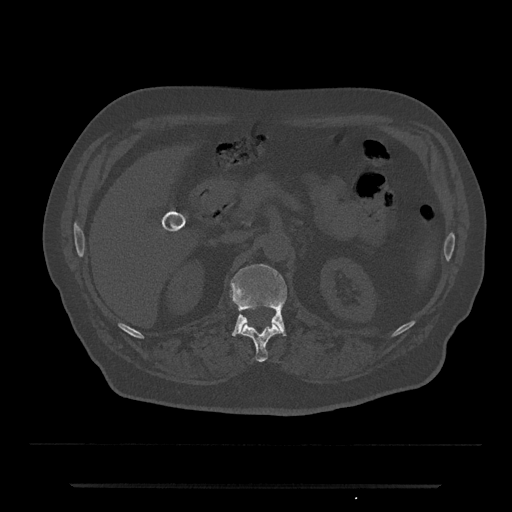
CT including the spine, one axial slice. Reconstruction kernel Br40s/3. Bone window (W 1800 / L 400 HU). 512 × 512 image matrix, field of view 434 × 434 mm. Male patient, age 80 years. From the clinical record (not read from this slice): primary cancer: prostate; vertebrae with lytic lesions (as recorded): L1, T11.
Structures marked on this image (semi-automatically segmented with operator editing):
- L1 vertebra: bounding box (x1, y1, x2, y2) in pixels: (230, 264, 287, 338)
- T12 vertebra: (242, 324, 281, 362)